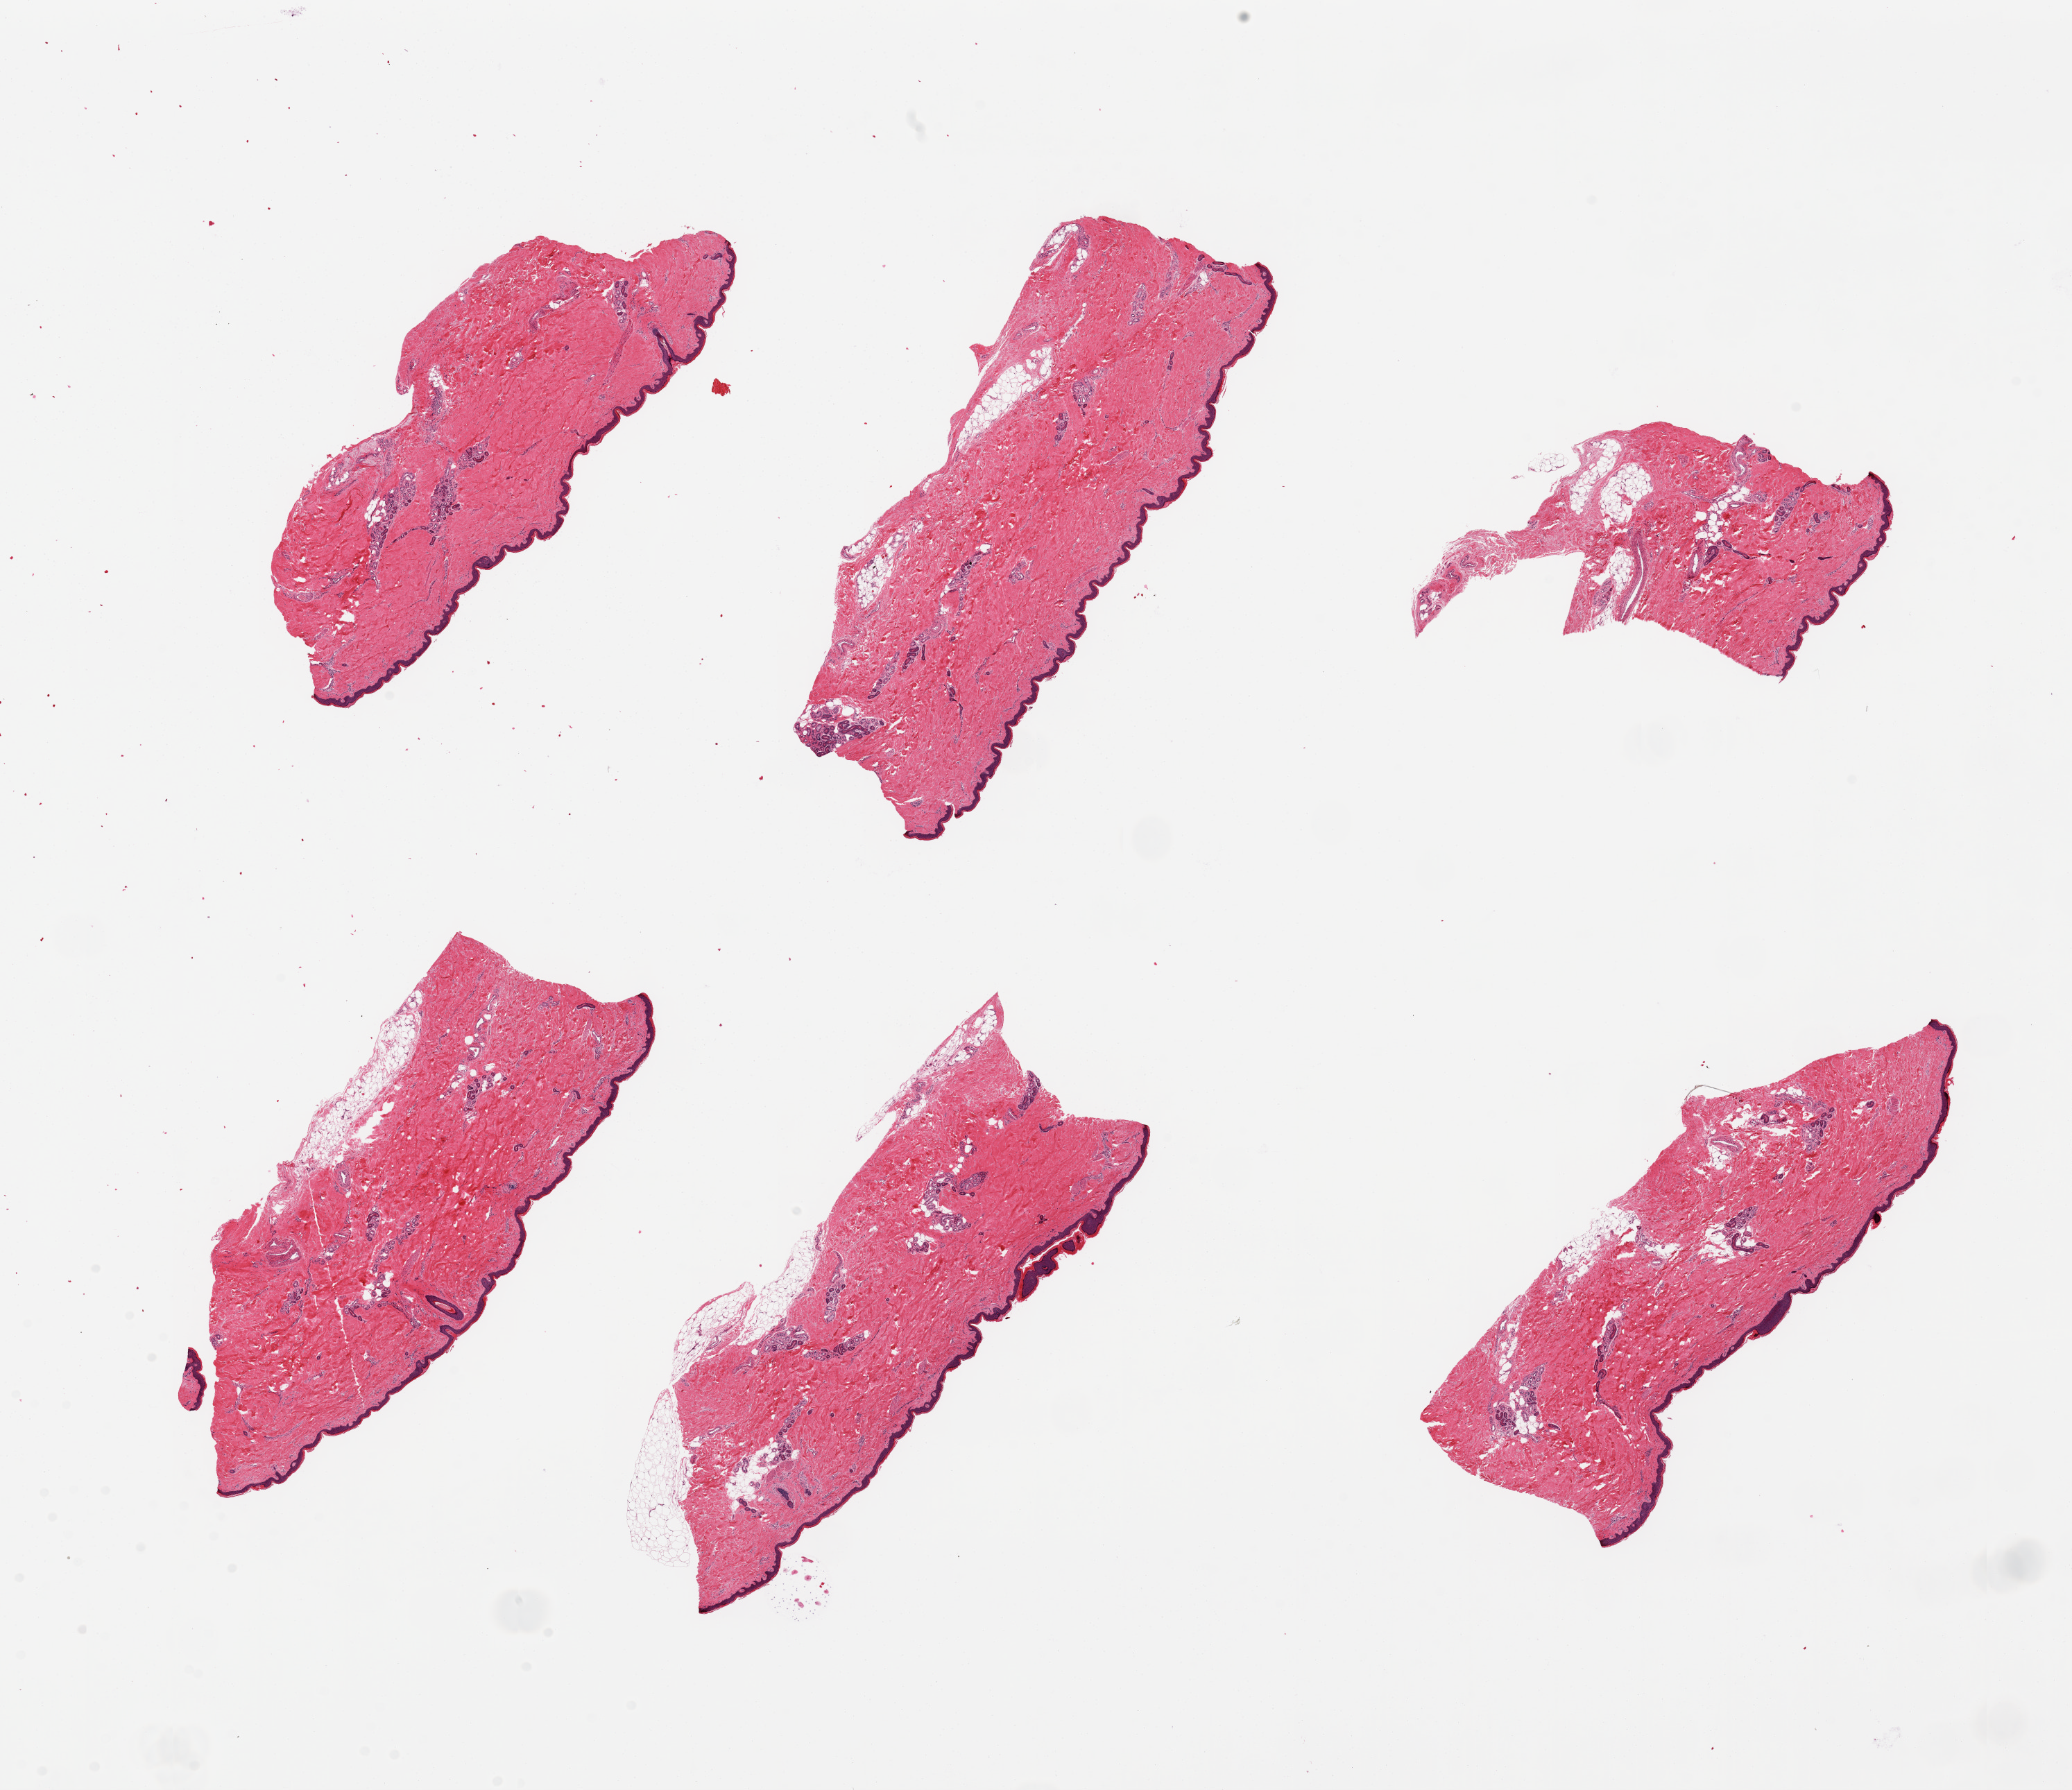
Haematoxylin and eosin whole-slide image, brightfield — whole scanned area (about 23.6 x 20.4 mm, acquisition: 20x scan) shown as a low-resolution overview, PAXgene-fixed paraffin-embedded (PFPE) section, section of skin of lower leg (target tissue), tissue donor sample.
Pathologist's review note for this sample: 6 pieces. up to 8x3mm; squamous epithelium is ~2-3% thickness.